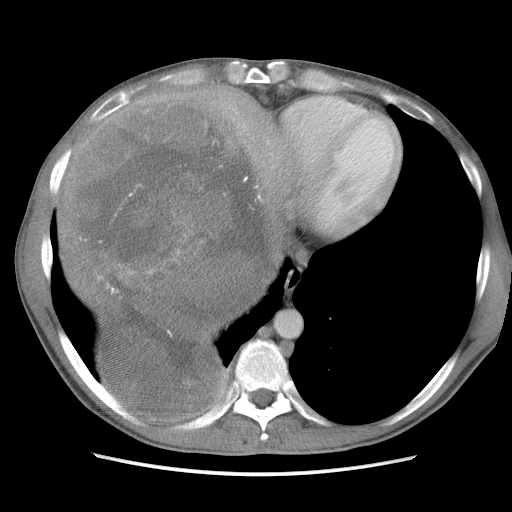
Contrast-enhanced abdominal CT, one axial slice; soft-tissue window (W 400 / L 40 HU); 5 mm slice thickness; 512 × 512 image matrix, field of view 360 × 360 mm. Male patient. From the clinical record (not read from this slice): diagnosis: adrenocortical carcinoma; tumour side: right adrenal; Ki-67 index: 13 %; stage (as recorded): 3.
Outlined on this slice (semi-automatically segmented with operator editing):
- mass: bounding box (x1, y1, x2, y2) in pixels: (66, 91, 288, 414)